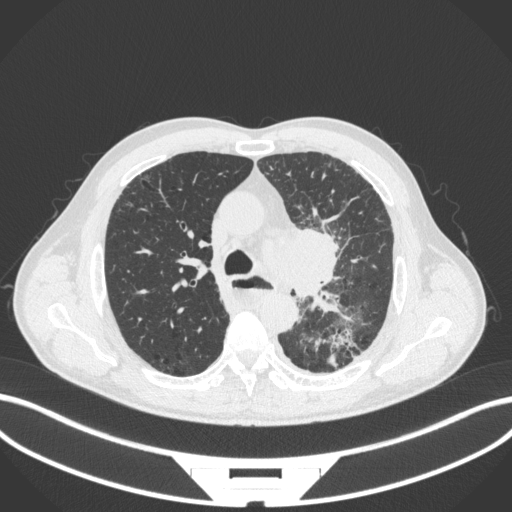
Chest CT, one axial slice; position 262 of 411 along the scan axis; 120 kVp; lung window (W 1500 / L -600 HU); 1 mm slice thickness; 512 × 512 image matrix, field of view 400 × 400 mm. Patient: male, 57 years. From the clinical record (not read from this slice): clinical TNM (as recorded): T2a N1 M0.
Outlined on this slice (bounding box drawn by a radiologist):
- lung tumour (recorded histology: squamous cell carcinoma): bounding box <265,220,347,303> (left, top, right, bottom; pixels)